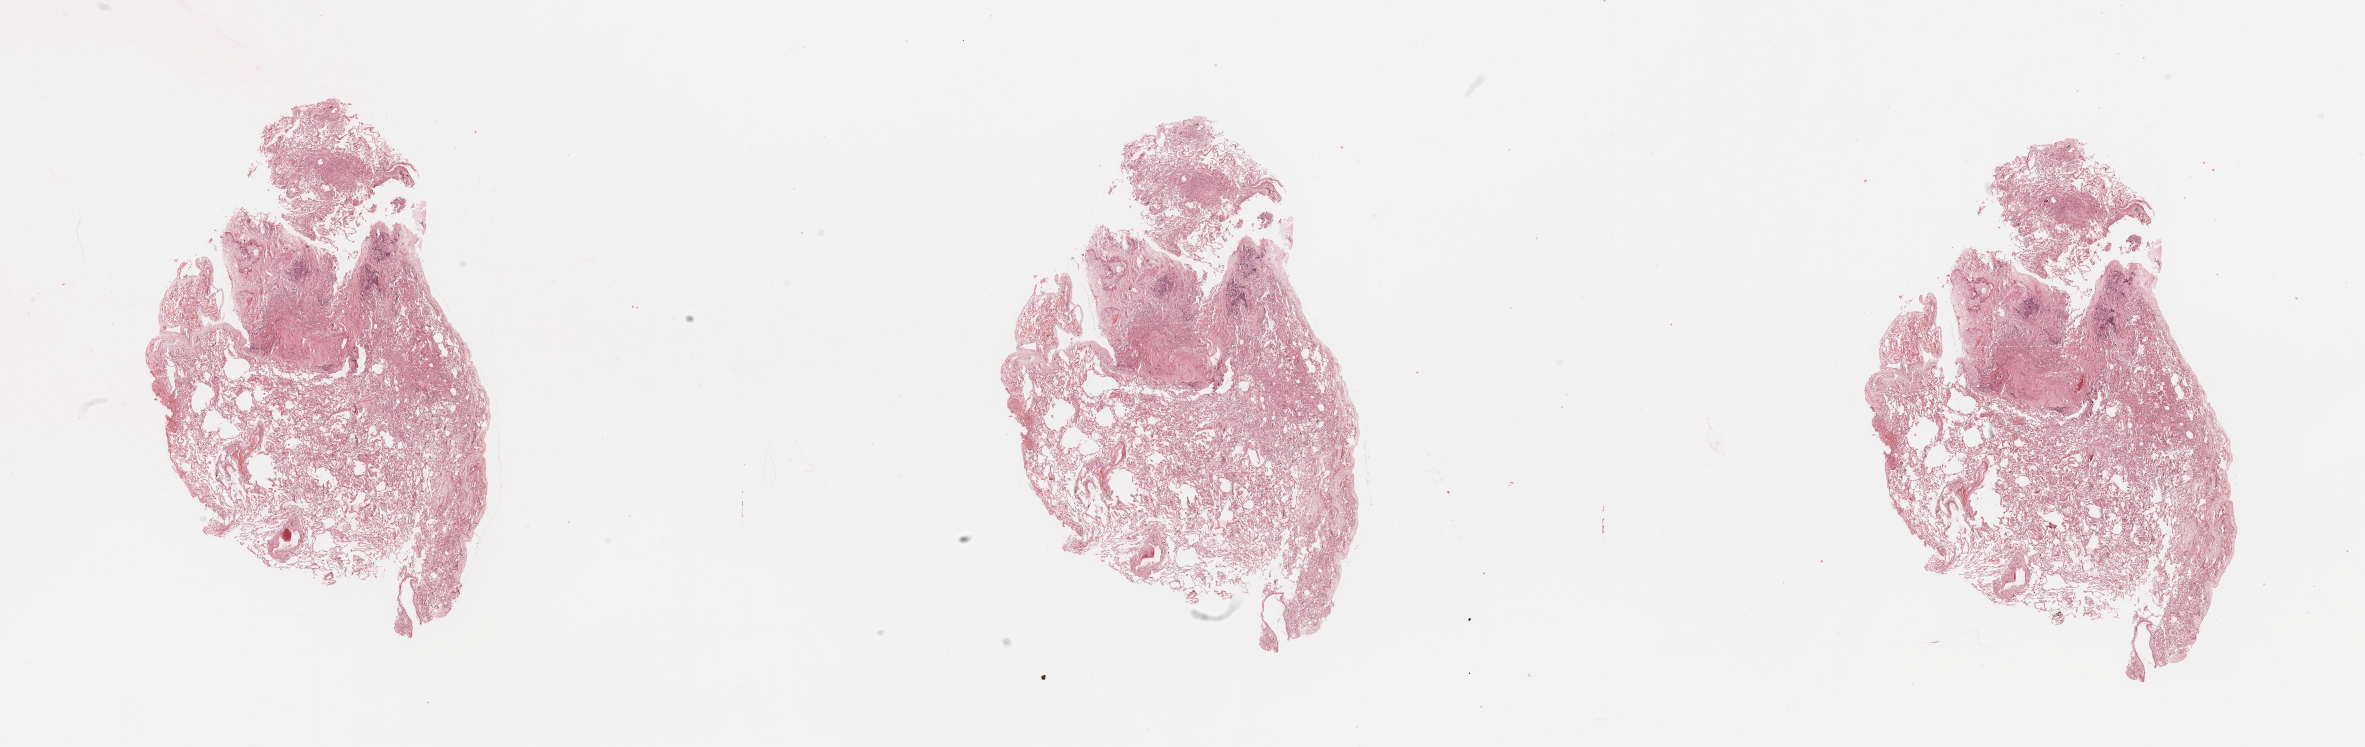
H&E whole-slide image — shown as a low-resolution overview of the whole scanned area (about 37.4 x 11.8 mm, slide scanned at 20x), lung, normal (non-tumour) tissue. Patient: male, age 71 years.
This section: normal (non-tumour) tissue from the same patient. Patient diagnosis (cohort enrolment): squamous cell carcinoma (lung).